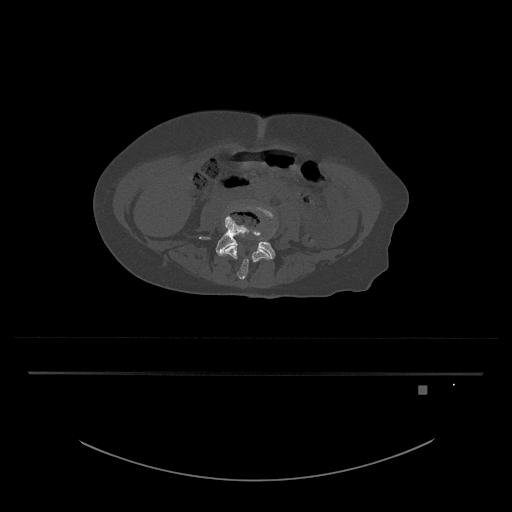
CT including the spine, one axial slice. Slice 333 of 797 in the series (ordered by position). 120 kVp. Bone window (W 1800 / L 400 HU). 0.5 mm slice thickness. 512 × 512 image matrix. Patient: female, 57 years. Case-level facts recorded for this patient, not image findings: primary cancer: cervical.
Outlined on this slice (semi-automatically segmented with operator editing):
- L4 vertebra: bounding box (x1, y1, x2, y2) in pixels: (220, 205, 274, 280)